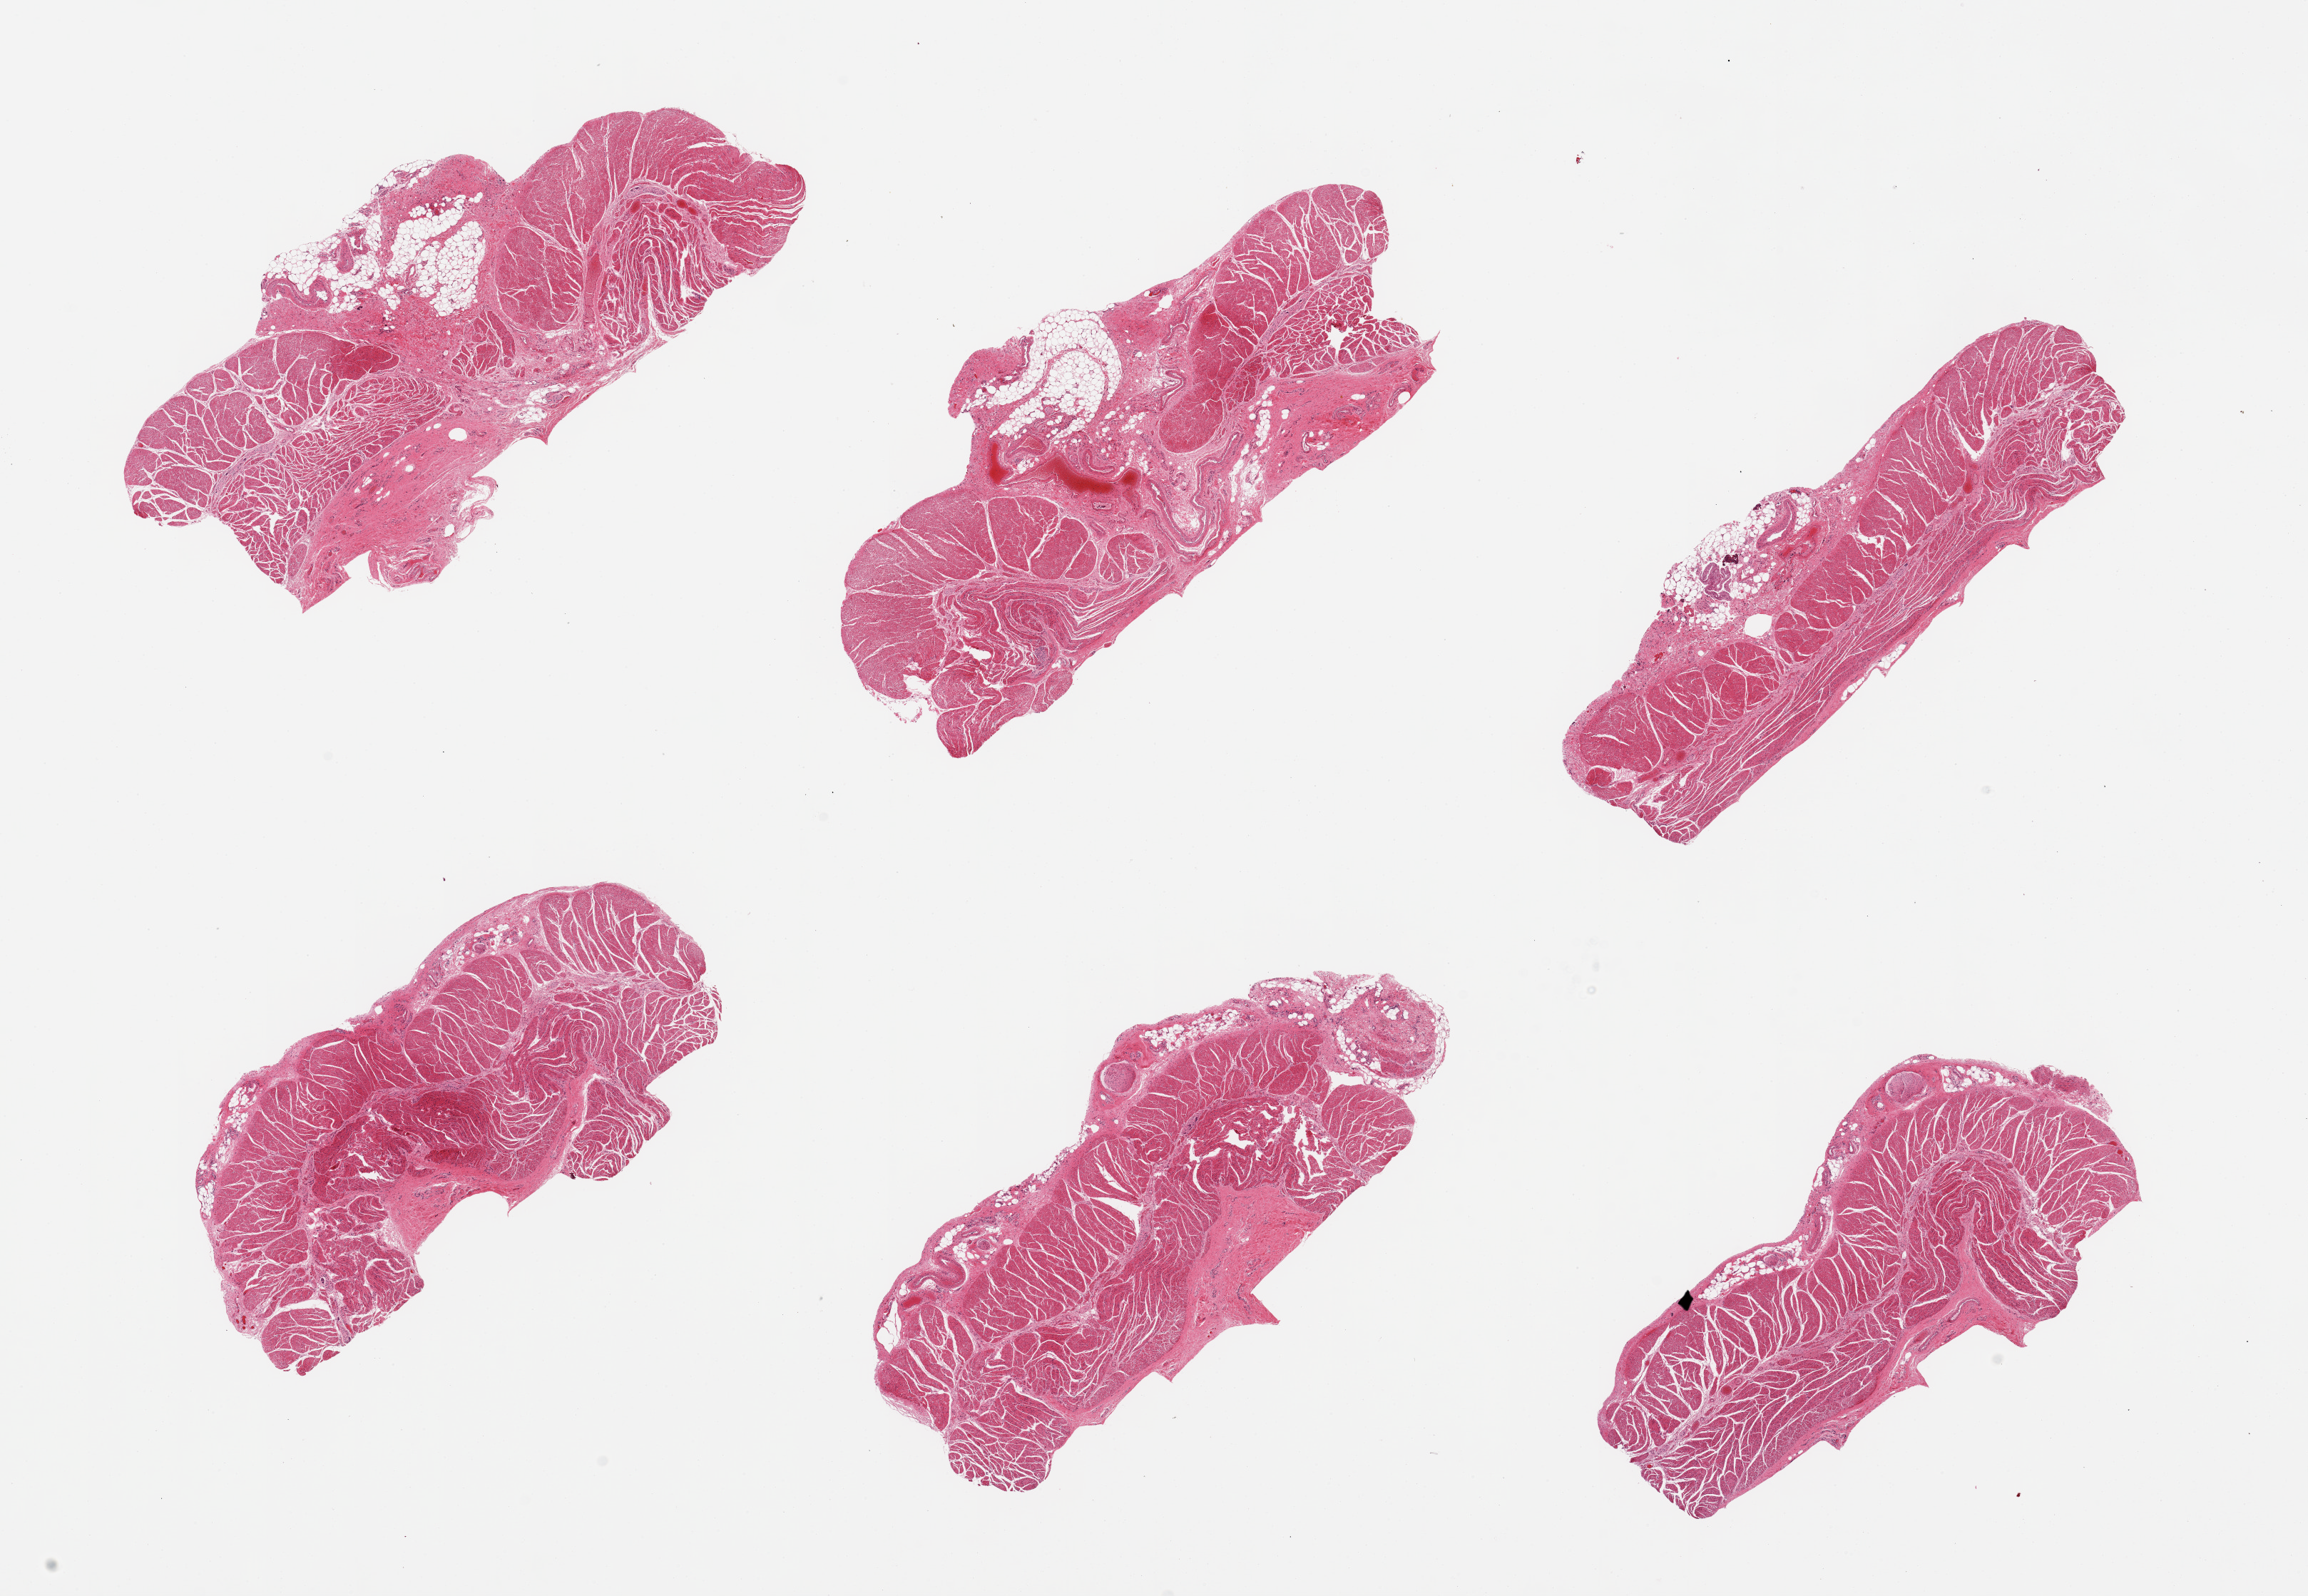
Hematoxylin and eosin (H&E) whole-slide image, brightfield, a low-resolution overview of the entire scanned area, about 25.6 x 17.7 mm (from a 20x scan). PAXgene-fixed paraffin-embedded (PFPE) section. Sampled site (target tissue): esophageal muscle. Tissue donor sample. Male donor.
* pathologist's review note for this sample: 6 pieces; muscularis with some residual attached fat and nerve